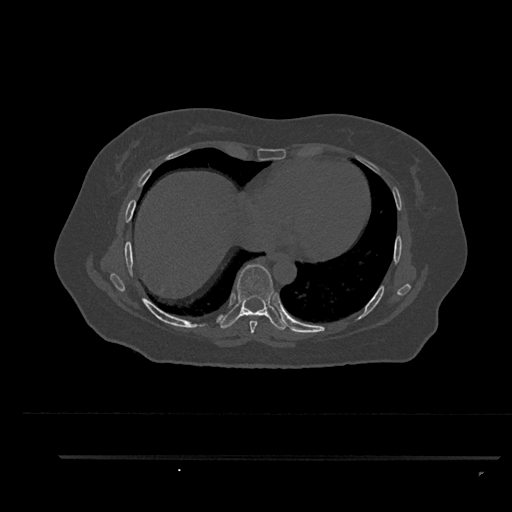
CT including the spine, one axial slice; slice 474 of 797 in the series (ordered by position); reconstruction kernel Br40s/3; 120 kVp; bone window (W 1800 / L 400 HU); 0.5 mm slice thickness; 512 × 512 image matrix. Female patient, age 44 years. Case-level facts recorded for this patient, not image findings: primary cancer: renal; vertebrae with lytic lesions (as recorded): L1.
Outlined on this slice (semi-automatic segmentation, software-assisted and operator-edited):
- T7 vertebra: box from (x=249, y=320) to (x=258, y=334) px
- T8 vertebra: (x=220, y=264)–(x=287, y=330)